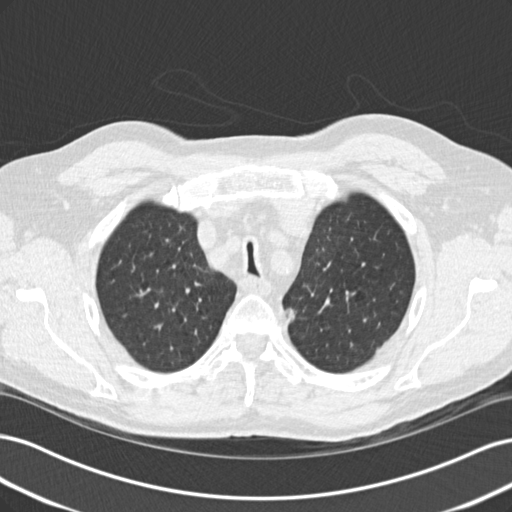
Chest CT (low-dose screening protocol), one axial image; first (baseline) screen; lung window (W 1500 / L -600 HU); 2 mm slice thickness; 120 kVp; slice 37 of 206 in the series. Male participant, aged 70 years at enrolment.
• Lesion marked by an expert reader, bounding box [x1, y1, x2, y2] px = [269, 291, 311, 337].
• The screening reader recorded 3 non-calcified nodules or masses ≥4 mm on this exam (left upper lobe, left lower lobe, right upper lobe); which of them this box marks is not recorded.